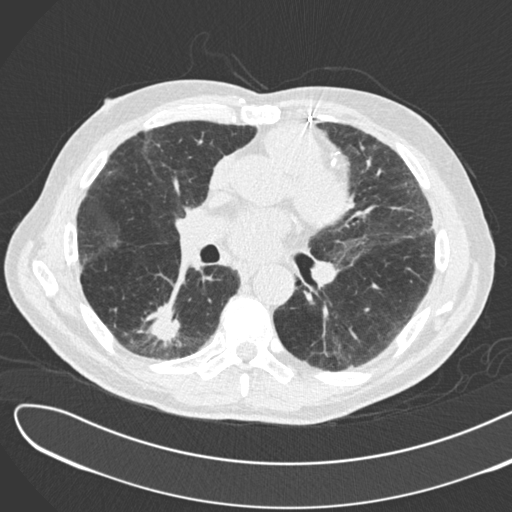
Axial slice from a low-dose chest CT screening exam, second screening round (one year after baseline), lung window (W 1500 / L -600 HU), 2 mm slice thickness, standard (soft-tissue) reconstruction kernel (B30f), 512 × 512 image matrix, field of view 370 × 370 mm. Male, age 72 years at enrolment. Former smoker at enrolment.
Lesion marked by an expert reader, bounding box [x1, y1, x2, y2] px = [132, 291, 194, 351]. The screening reader recorded 2 non-calcified nodules or masses ≥4 mm on this exam; which of them this box marks is not recorded. Official screen result: positive, change unspecified: nodule(s) >= 4 mm or enlarging nodule(s), mass(es), or other non-specific abnormalities suspicious for lung cancer. Lung cancer was diagnosed 46 days after this screen: squamous cell carcinoma, NOS, right lower lobe, poorly differentiated (G3), stage IB (AJCC 6th edition), 42 mm at pathology.